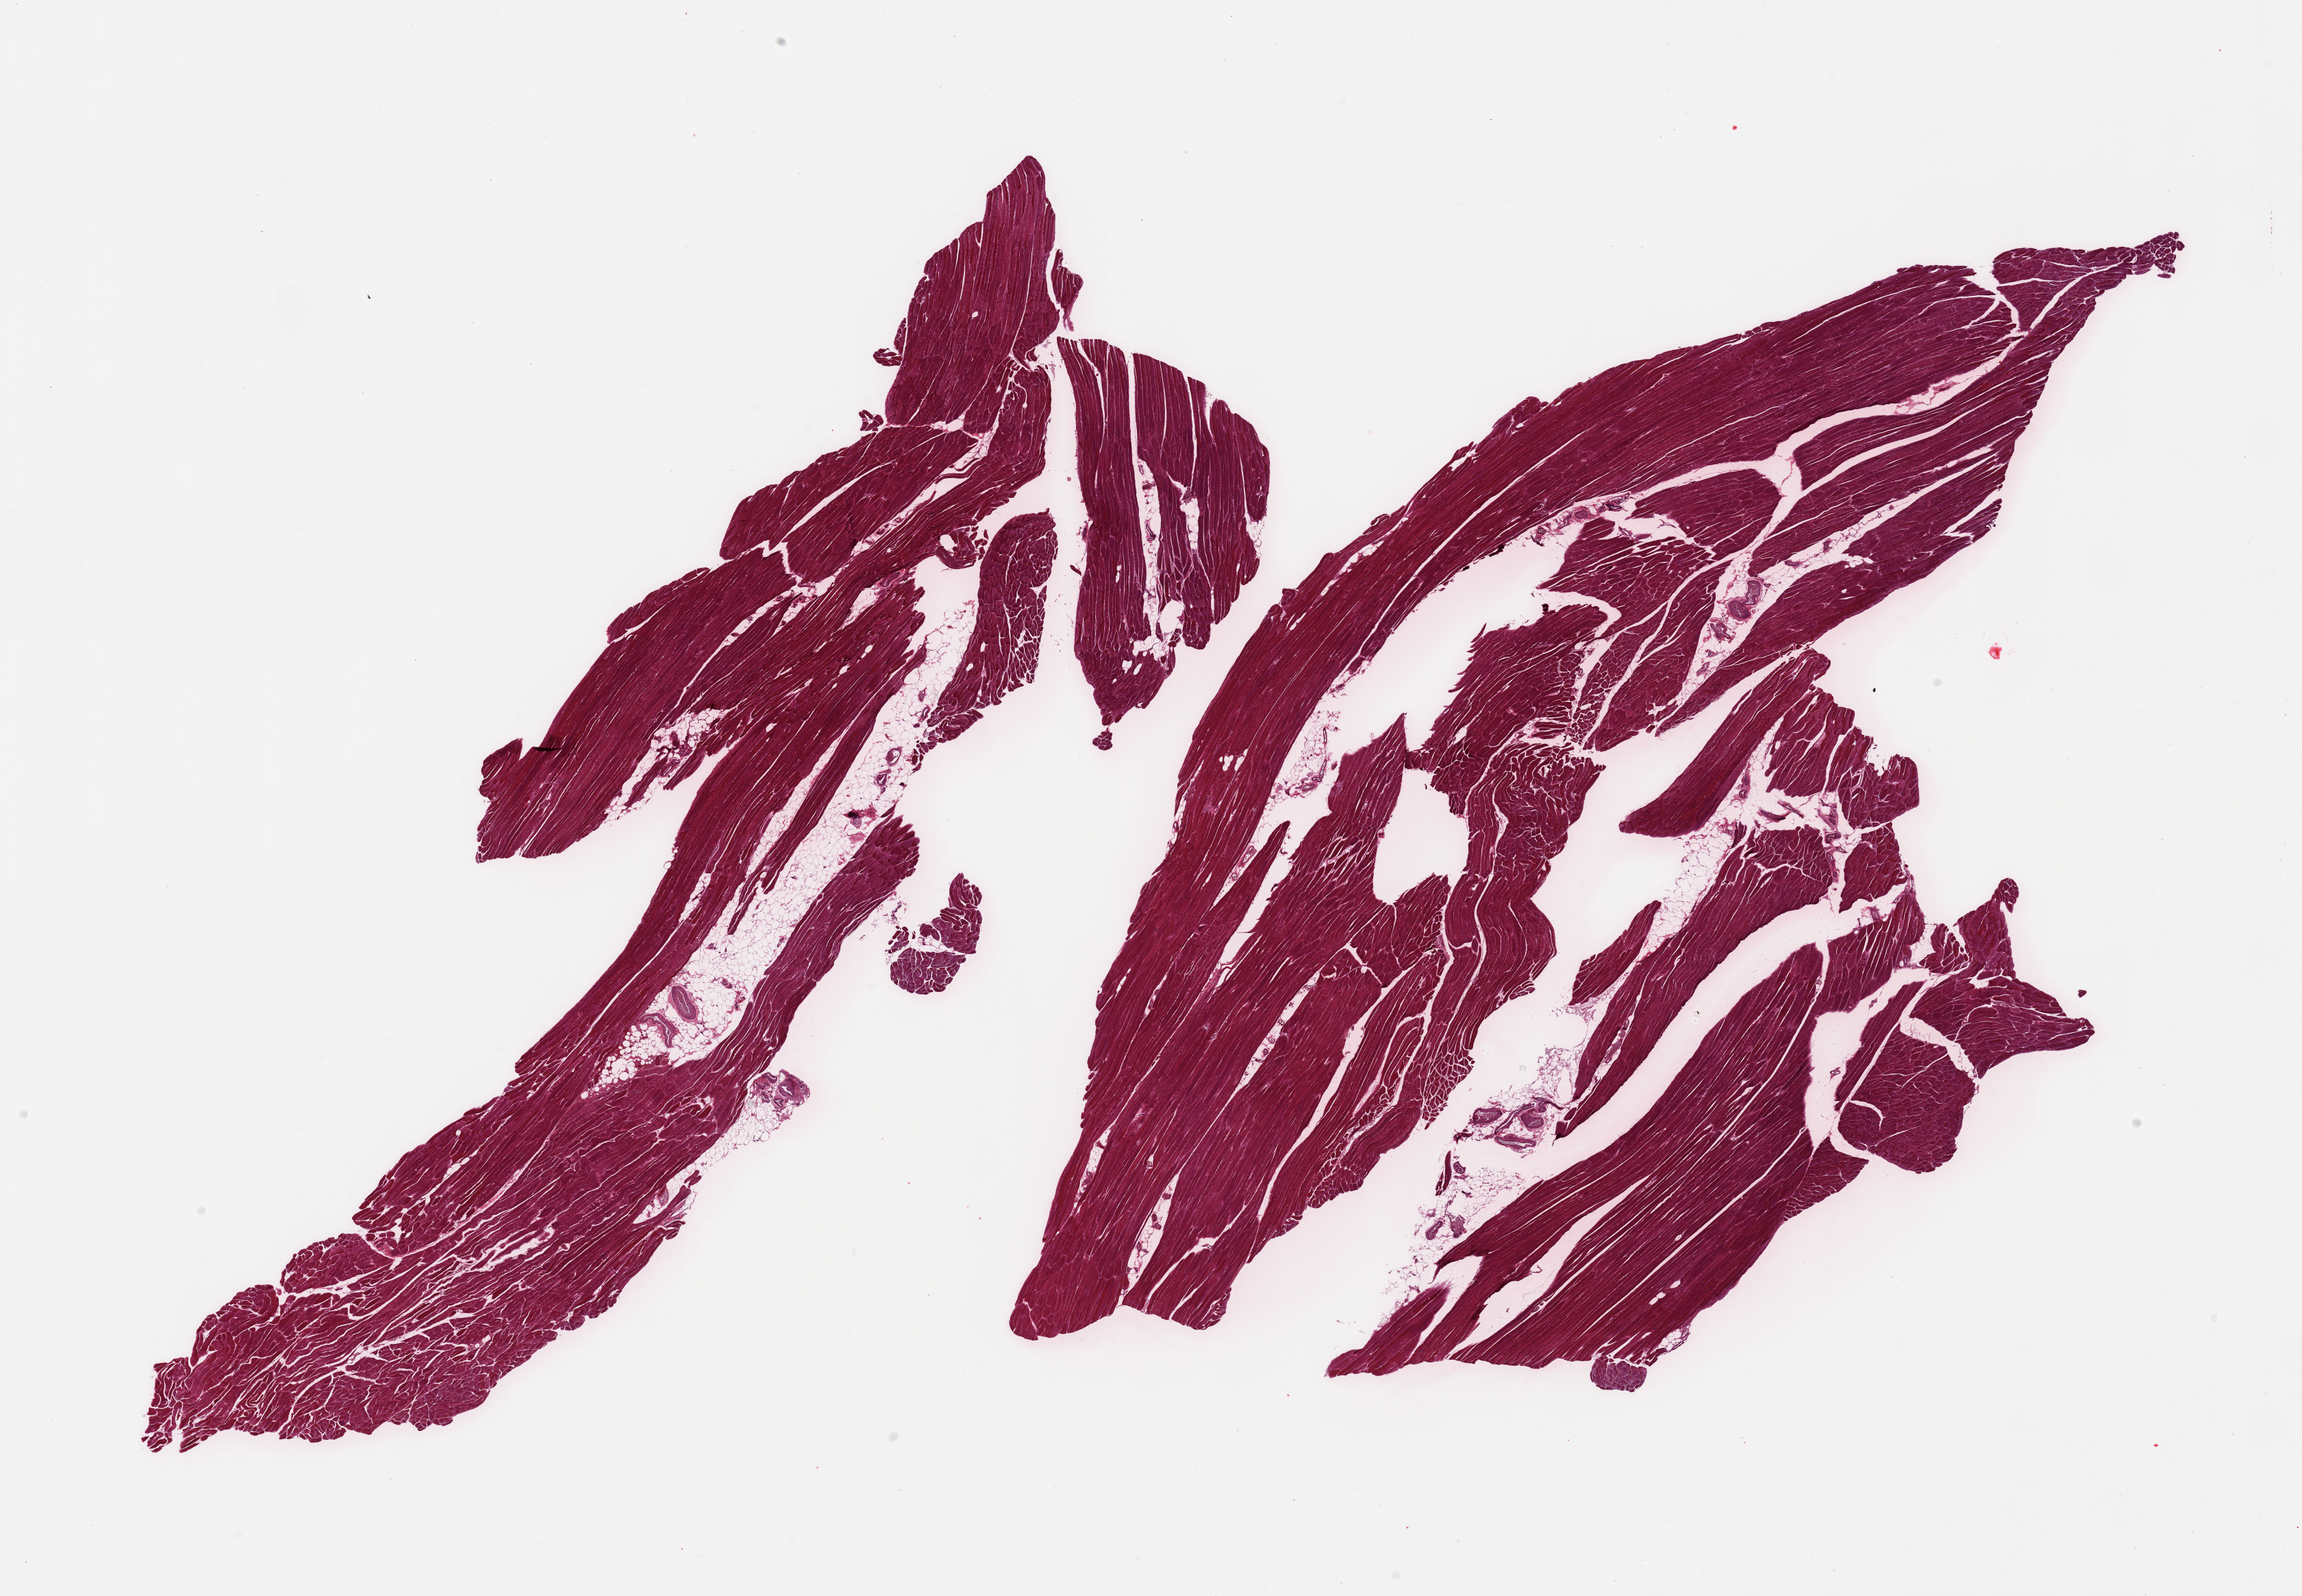
Digitized H&E-stained section, a low-resolution overview of the entire scanned area, about 26.6 x 18.4 mm; PAXgene-fixed, paraffin-embedded tissue; sampled site (target tissue): skeletal muscle; donor tissue sample.
Review note (as recorded): 2 pieces; skeletal muscle with at least 10% internal fat (1 piece is incomplete section).